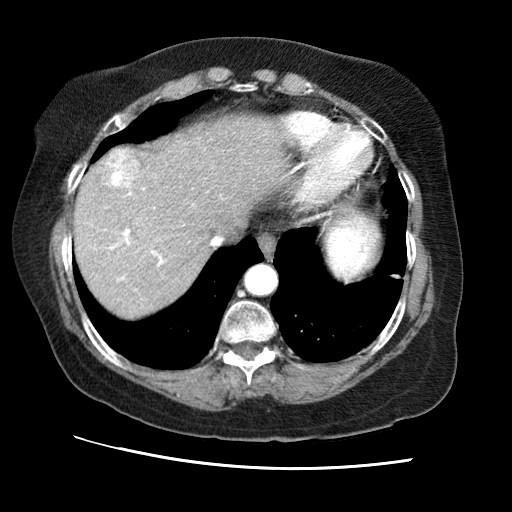
Contrast-enhanced abdominal CT (liver protocol), one axial slice; slice 57 of 65 in the series (ordered by position); soft-tissue window (W 400 / L 40 HU); 2.5 mm slice thickness; 512 × 512 image matrix, field of view 340 × 340 mm. From the clinical record (not read from this slice): diagnosis: hepatocellular carcinoma (patient treated with transarterial chemoembolisation; whether this scan precedes or follows treatment is not stated here); TNM stage (as recorded): Stage-II; Child-Pugh class: A; tumour size: 2.5 cm.
Outlined on this slice (semi-automatically segmented with operator editing):
- abdominal aorta: bounding box (x1, y1, x2, y2) in pixels: (247, 266, 276, 294)
- liver parenchyma outside the tumour (the mass and vessels are separate outlines, so this box may not span the whole liver): (74, 116, 287, 317)
- mass: (95, 148, 146, 190)
- liver vessels: (94, 186, 165, 281)